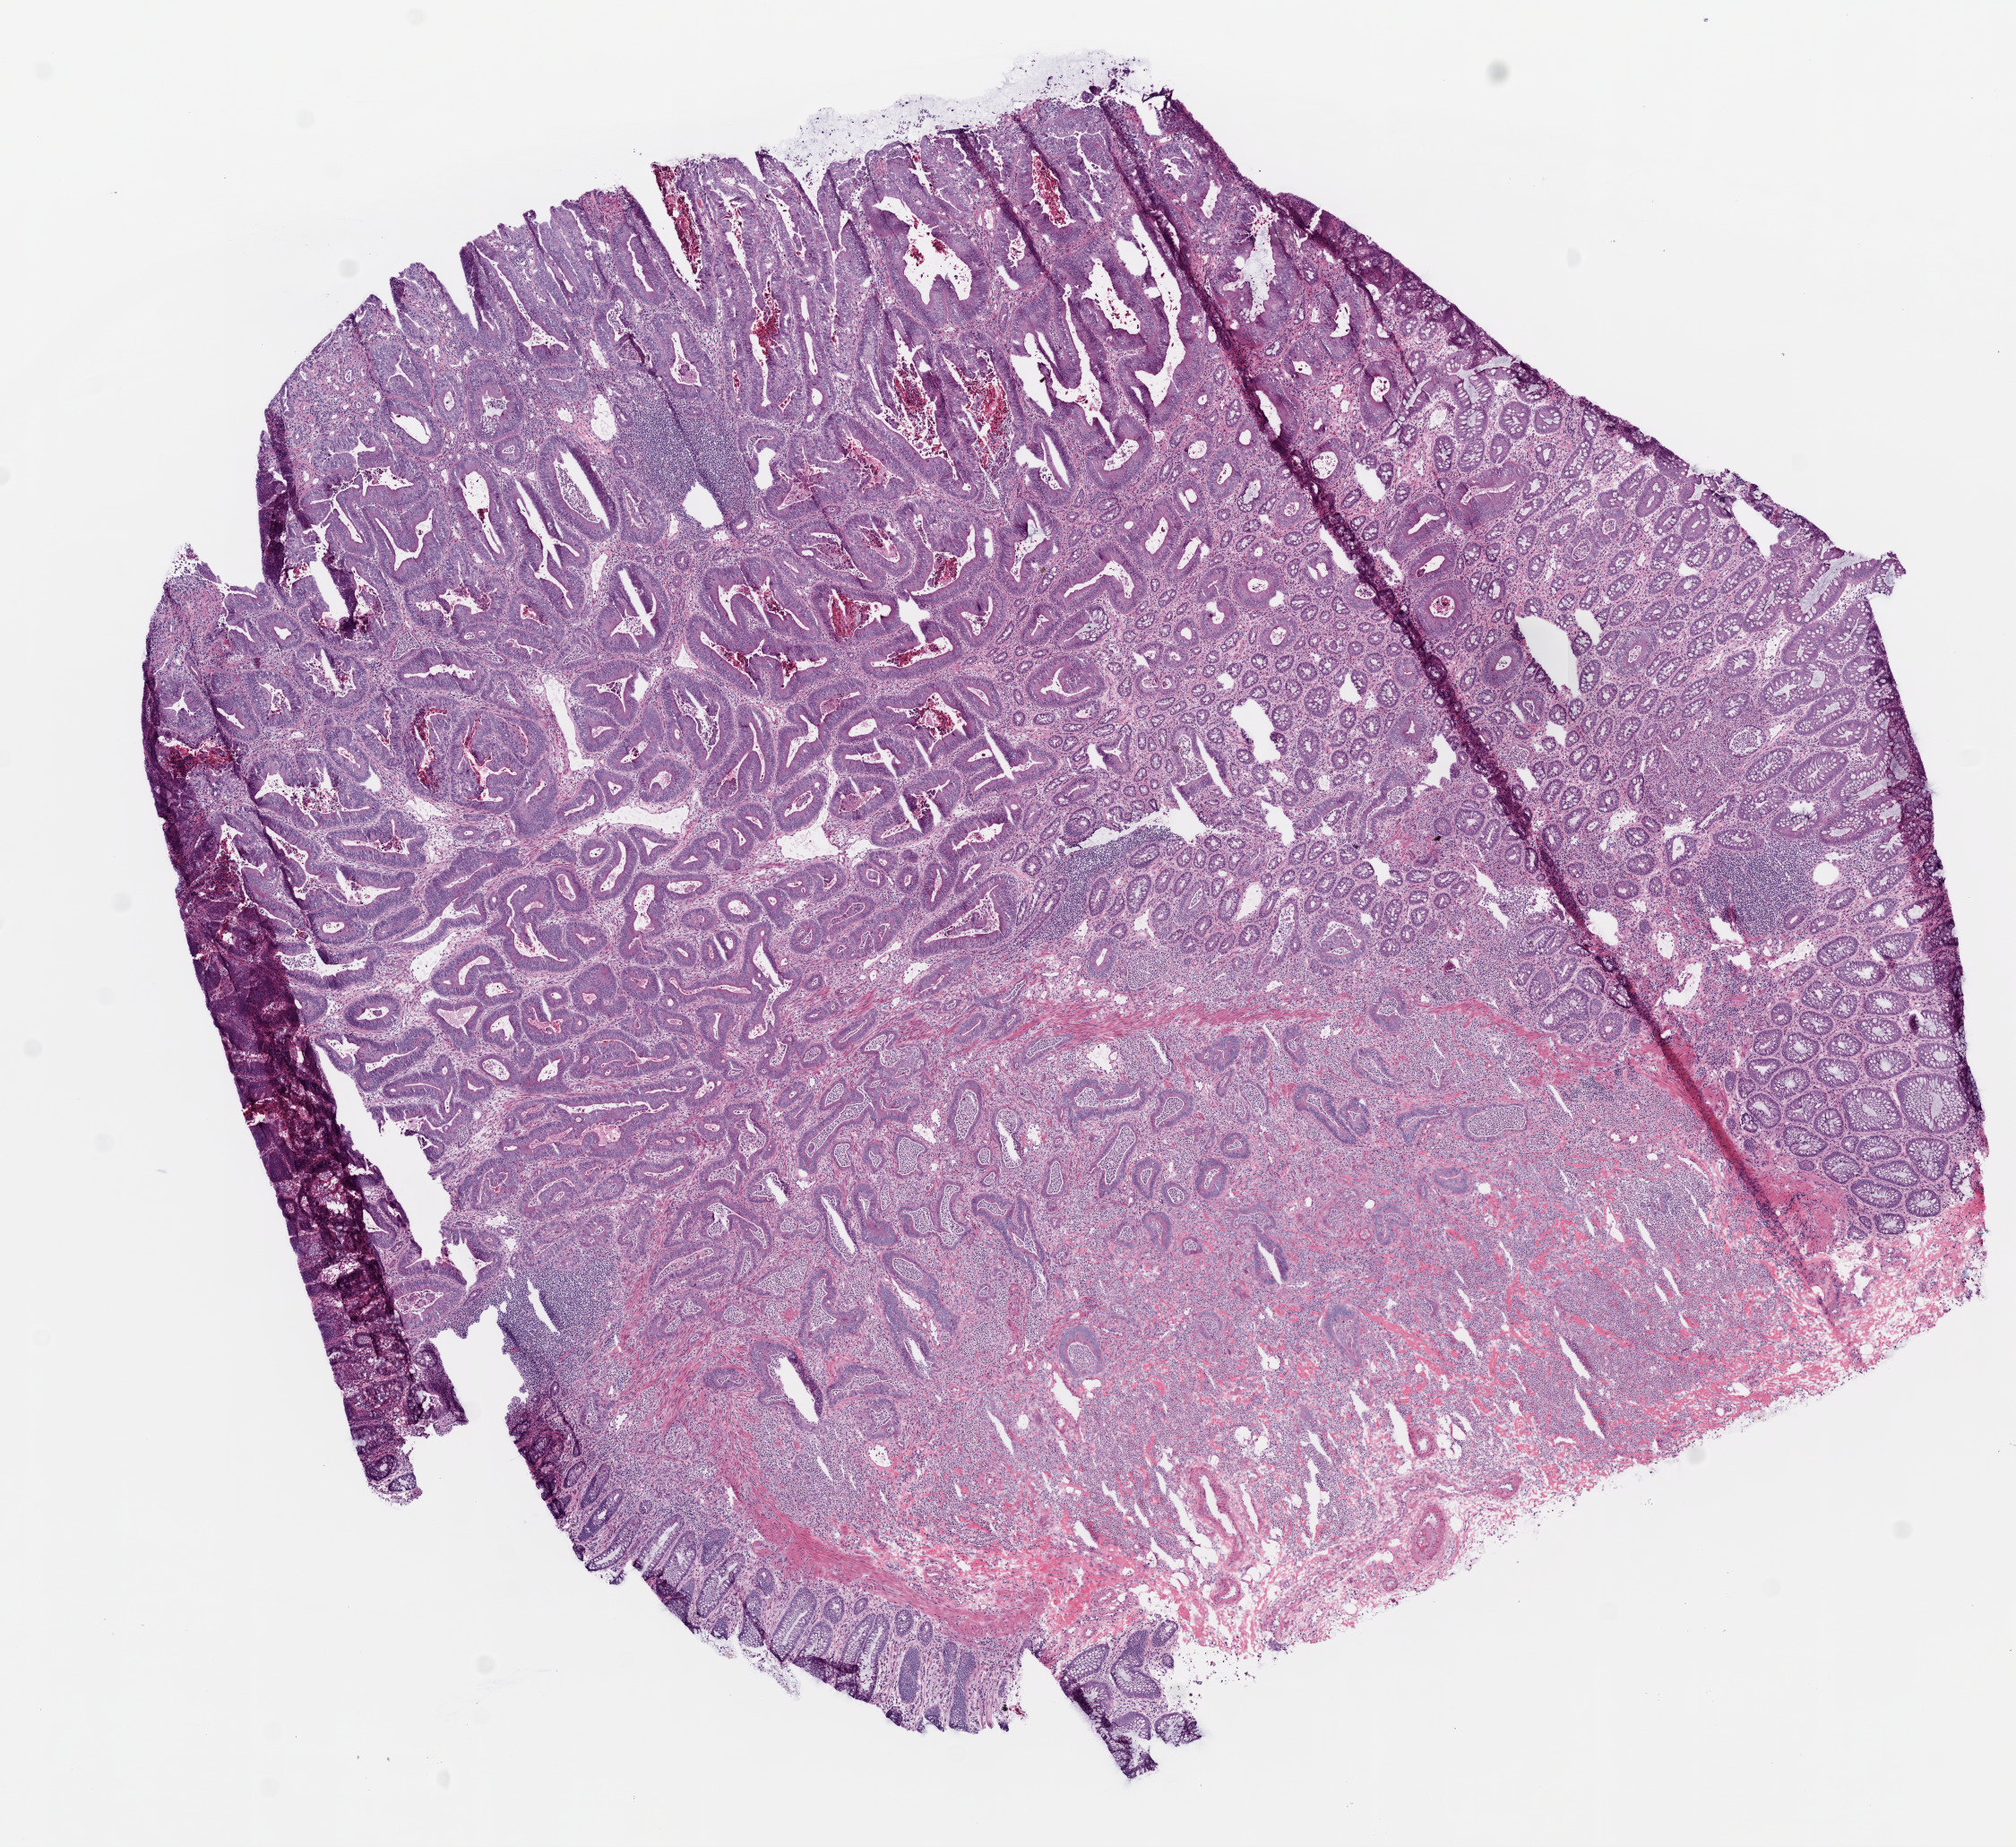
Whole-slide histology image, Hematoxylin and eosin (H&E) stained — whole scanned area (about 9.0 x 8.3 mm, from a 20x scan) shown as a low-resolution overview, frozen section from the bottom of the tissue portion, primary tumour sample from the colon. Patient: female, age at initial diagnosis 53 years.
Pathologic diagnosis: Adenocarcinoma, NOS (sigmoid colon).